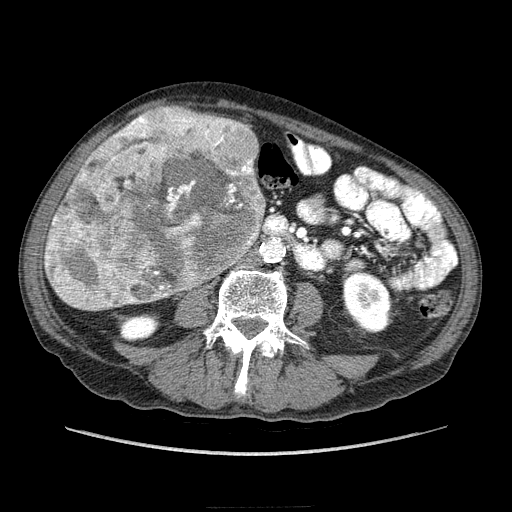
Contrast-enhanced abdominal CT (liver protocol), one axial slice; position 63 of 218 along the scan axis; soft-tissue window (W 400 / L 40 HU); 512 × 512 image matrix, field of view 380 × 380 mm. From the clinical record (not read from this slice): diagnosis: hepatocellular carcinoma (patient treated with transarterial chemoembolisation; whether this scan precedes or follows treatment is not stated here); TNM stage (as recorded): Stage-IIIA.
Annotated regions visible in this slice (semi-automatically segmented with operator editing):
- liver parenchyma outside the tumour (the mass and vessels are separate outlines, so this box may not span the whole liver): box from (x=44, y=114) to (x=256, y=310) px
- mass: (x=45, y=106)–(x=267, y=311)